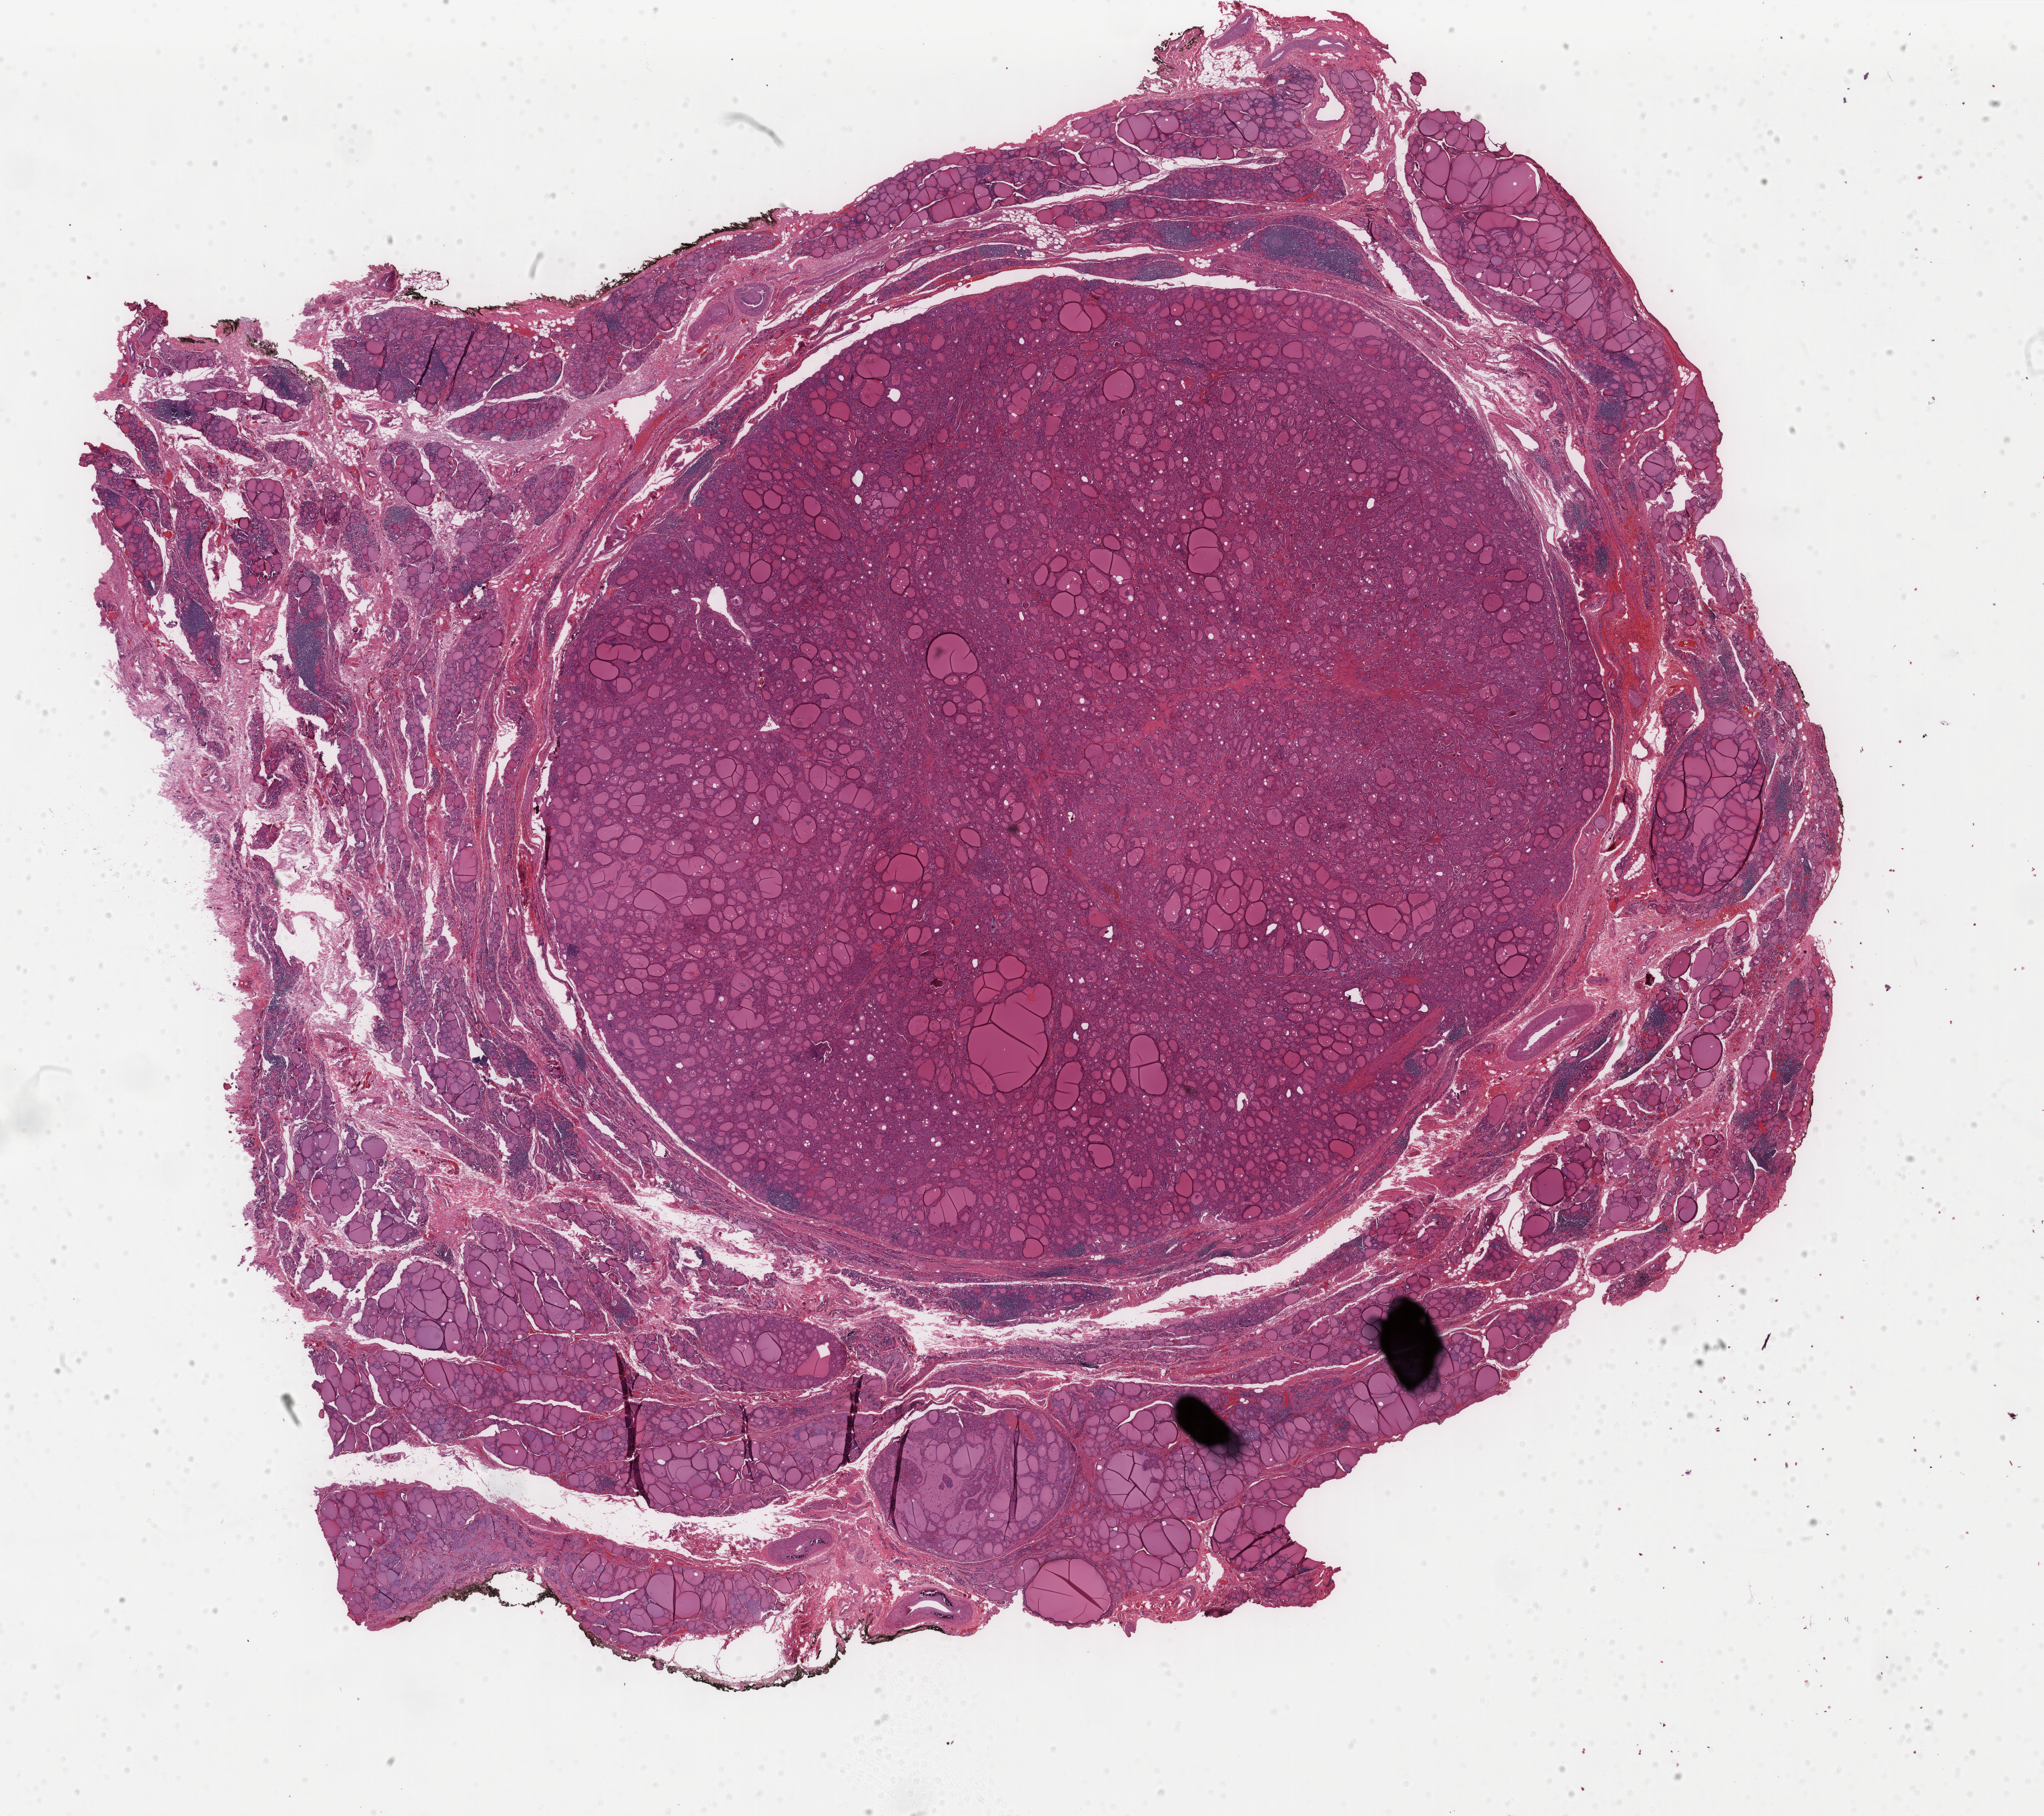
Whole-slide histology image, H&E, whole scanned area (about 24.3 x 21.6 mm, slide scanned at 40x) shown as a low-resolution overview; formalin-fixed paraffin-embedded (FFPE) diagnostic section; sample: primary tumour, thyroid. Male, age 77 years at initial diagnosis.
TNM: T3 N0 M0. AJCC pathologic stage: III (7th edition). Histologic diagnosis: Papillary adenocarcinoma, NOS (thyroid gland).